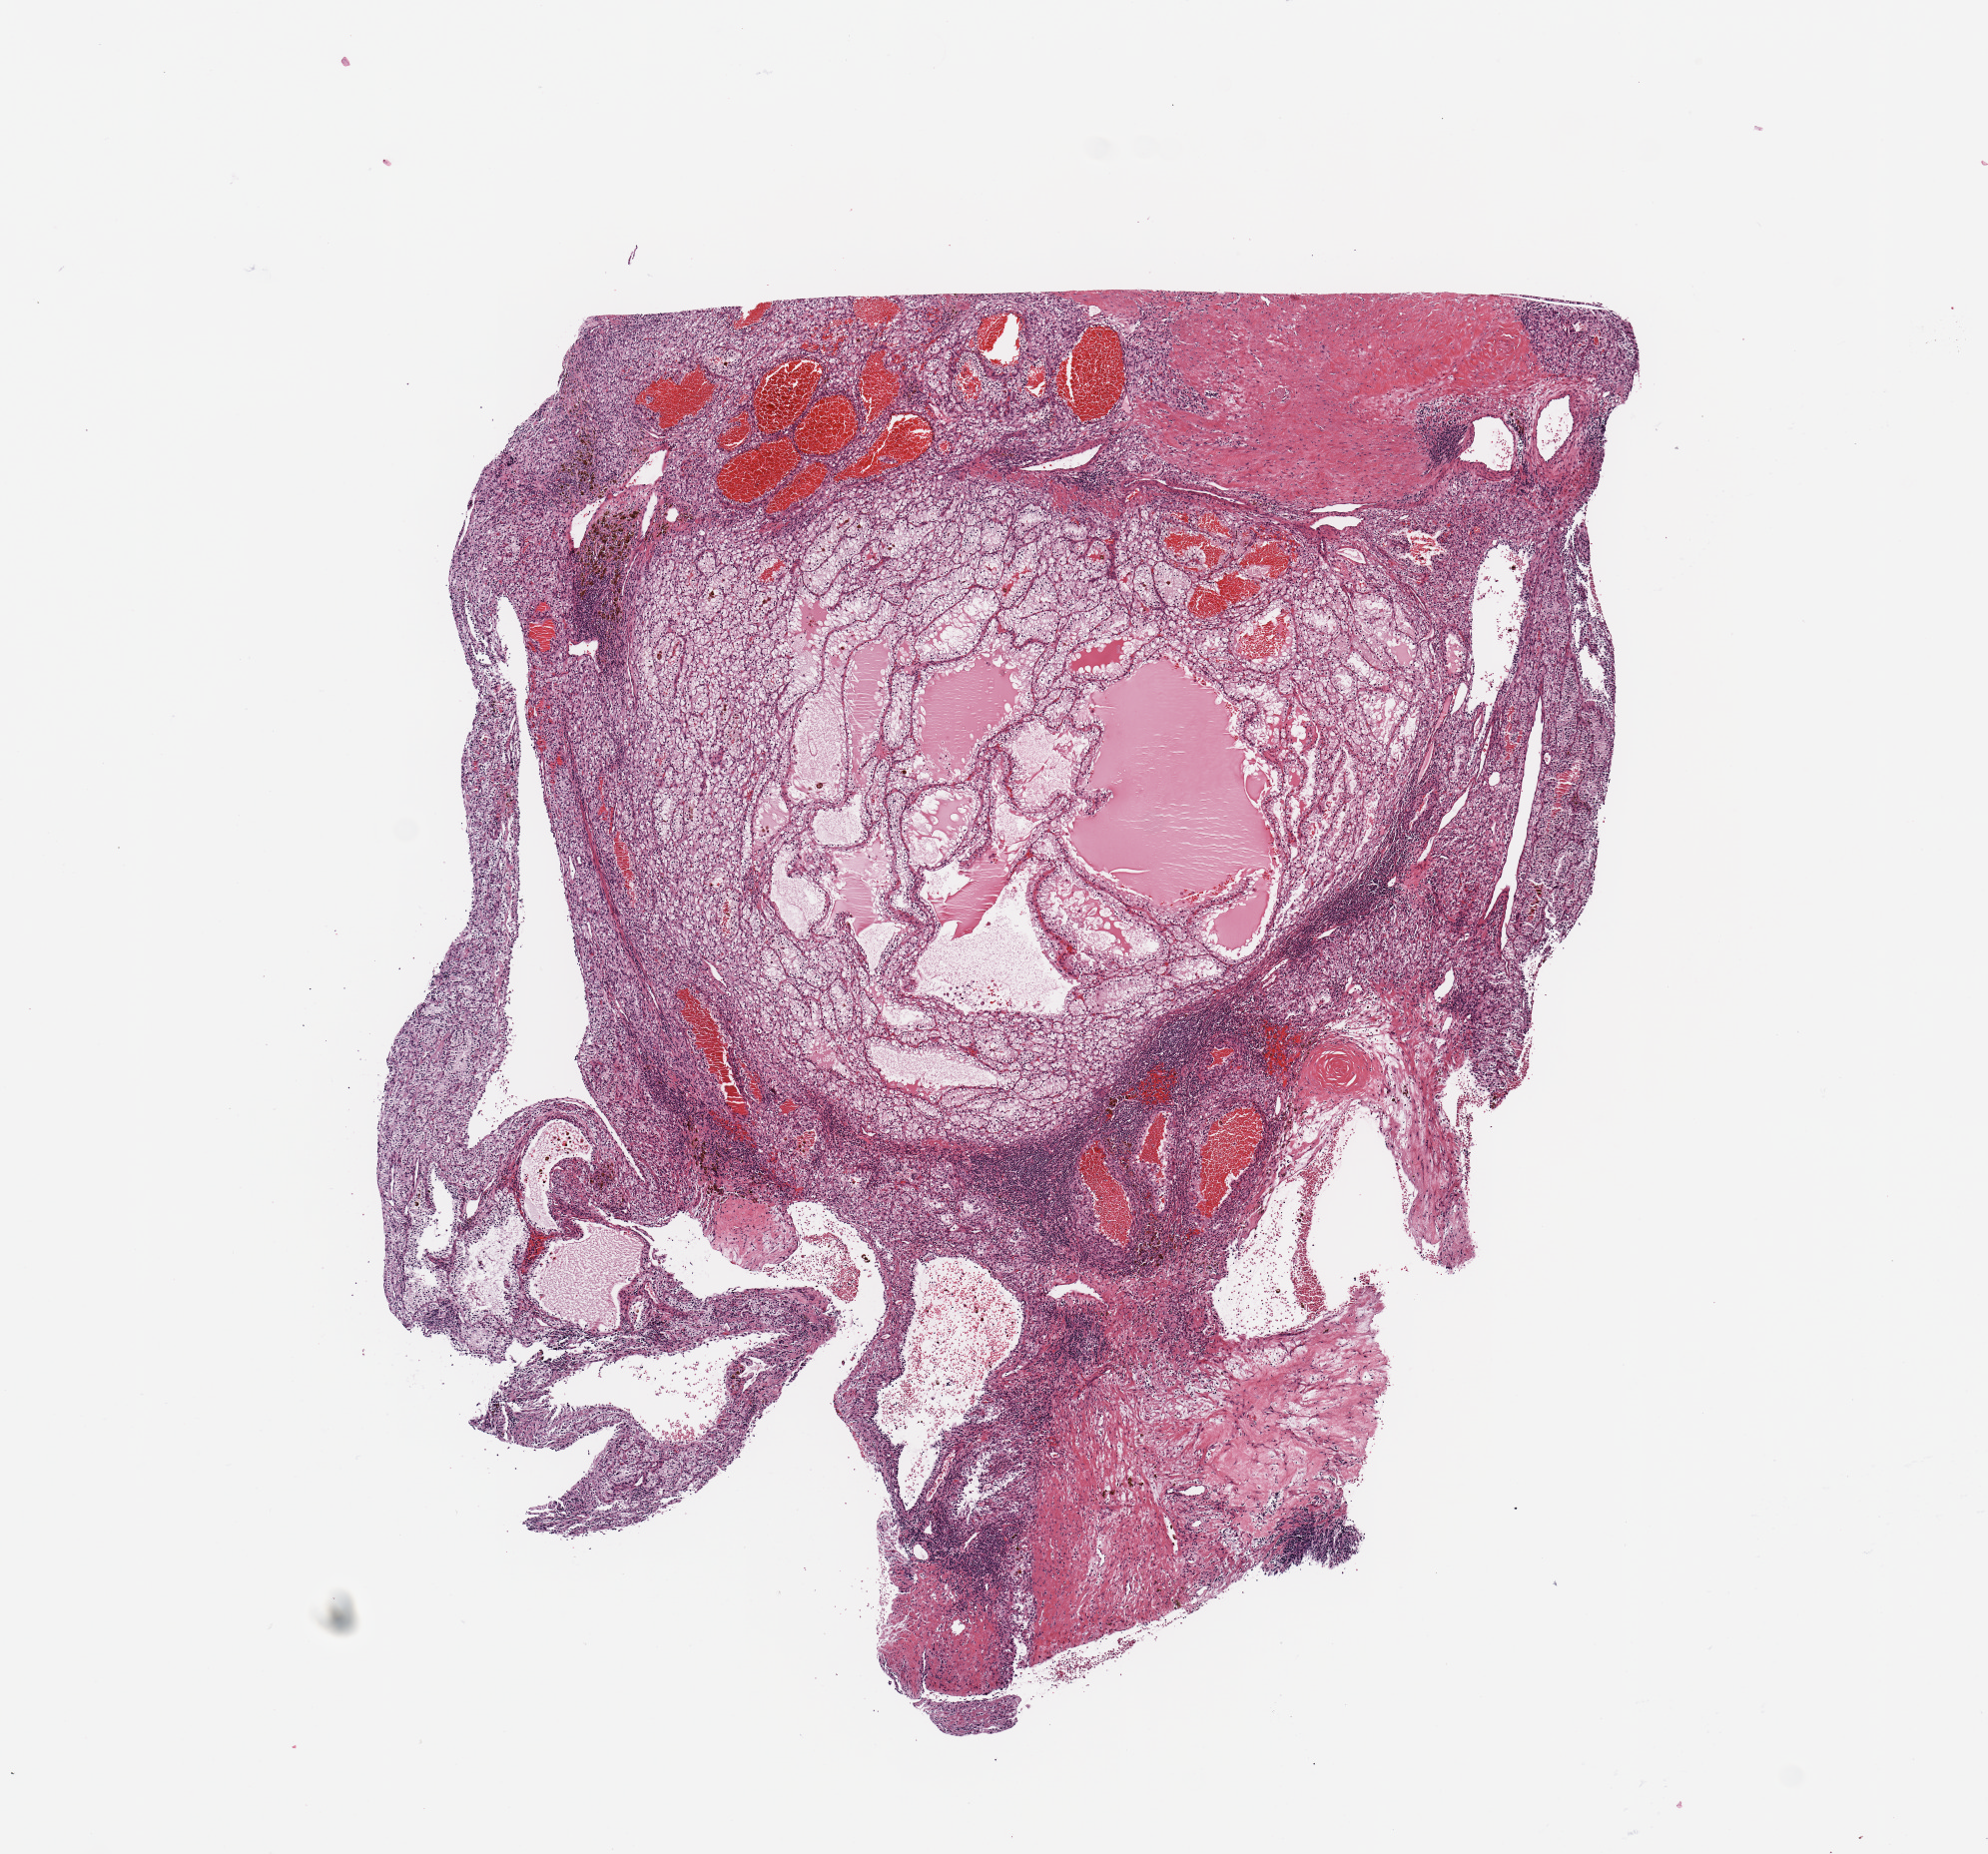
Whole-slide histology image, H&E — low-resolution overview of the scanned area, about 7.9 x 7.3 mm (acquisition: 20x scan). Tumour tissue sample, sampled site: kidney. 48-year-old female patient. Histologic grade: G1 (well differentiated). Pathologist review of this section (percent, as recorded): tumour nuclei 80%, necrosis 5%.
AJCC pathologic stage: I. Diagnosis: Renal cell carcinoma, NOS. Primary tumour site (as recorded): upper pole.